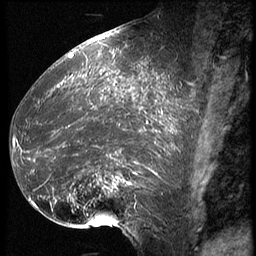
Breast MRI (dynamic contrast-enhanced), one sagittal slice. Slice 27 of 62 in the series (ordered by position). 3 images stored at this slice position (order not interpretable as contrast timing). 1.5 T. TE 4.2 ms, TR 9 ms. 2.5 mm slice thickness. 256 × 256 image matrix, field of view 180 × 180 mm. Female patient, age 39 years. Case-level facts recorded for this patient, not image findings: setting: breast cancer imaged before/during neoadjuvant chemotherapy; receptor status: HER2-positive.
Structures marked on this image (semi-automatic segmentation, software-assisted and operator-edited):
- analysis volume of interest (the breast-tissue region the enhancement analysis was run in; not a lesion): bounding box [x1, y1, x2, y2] px = [16, 64, 171, 228]
- tumour enhancement mask (voxels above the 140 % enhancement threshold inside the analysis volume of interest): [16, 73, 171, 204]